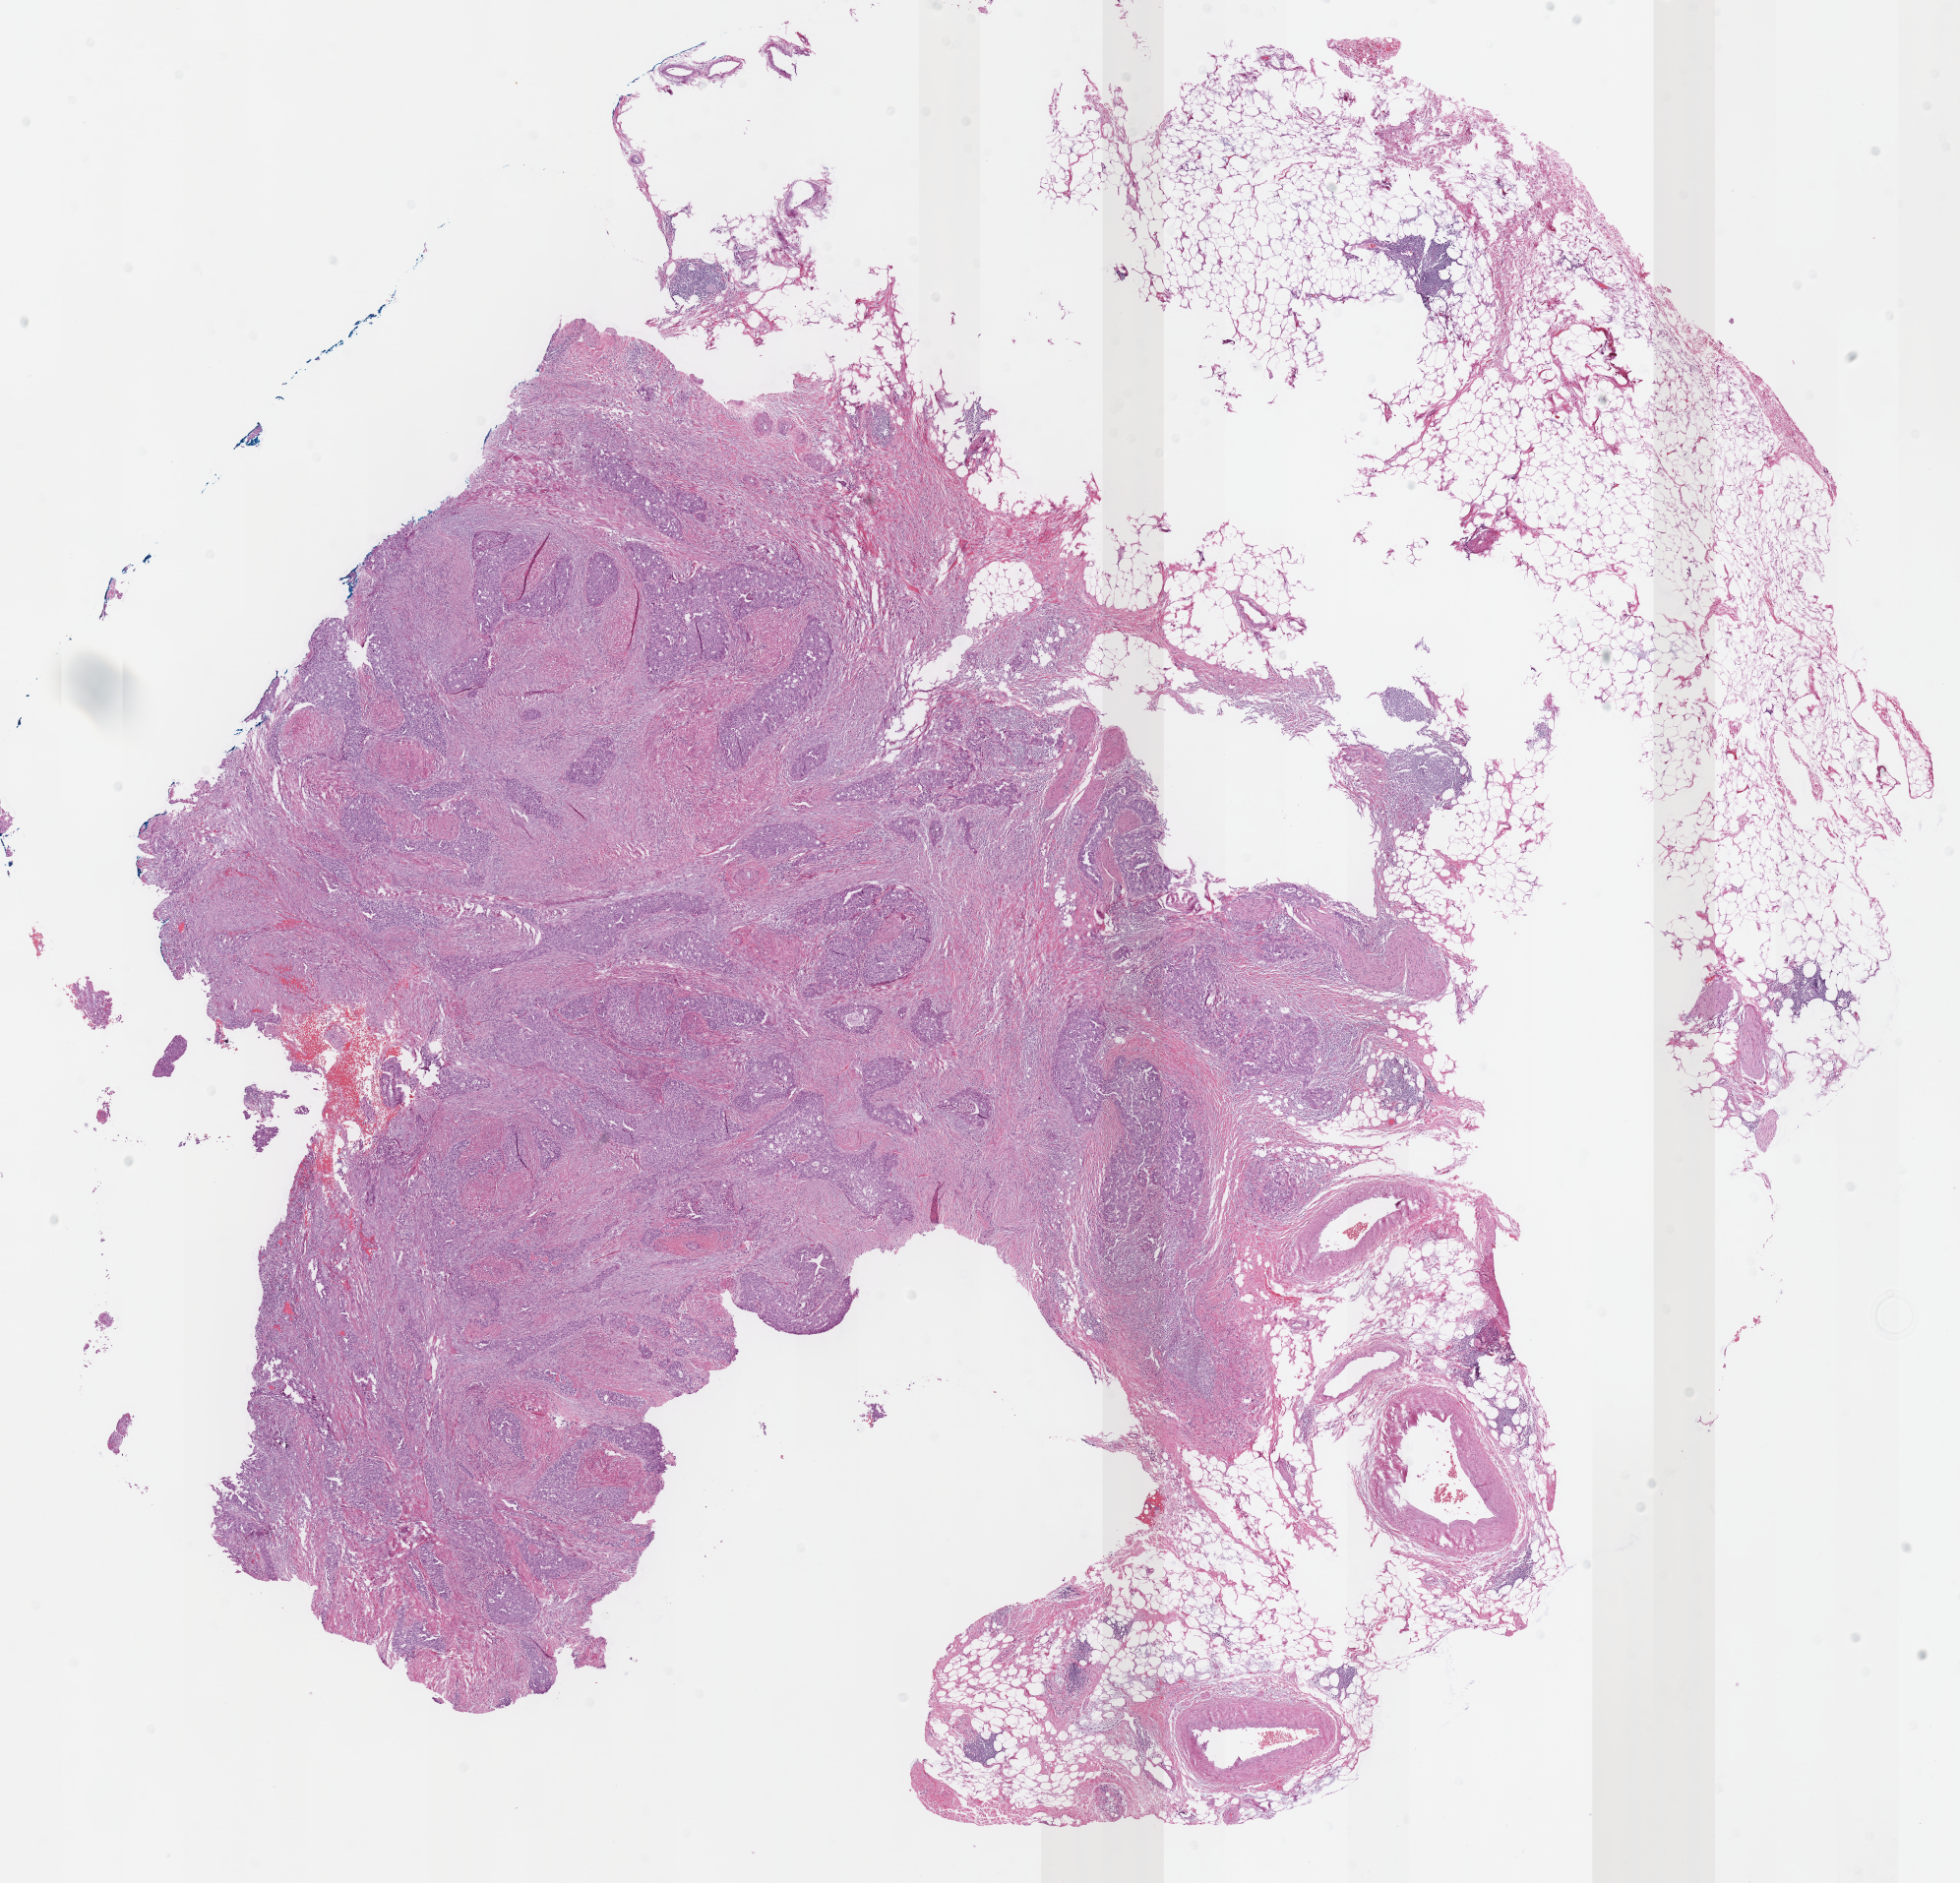
Digitized H&E-stained tissue section (whole slide) — a low-resolution overview of the entire scanned area, about 15.7 x 15.0 mm (slide scanned at 40x); formalin-fixed paraffin-embedded (FFPE) diagnostic section; primary tumour sample from the bladder. Male, age 79 years at initial diagnosis.
Diagnosis: Transitional cell carcinoma.